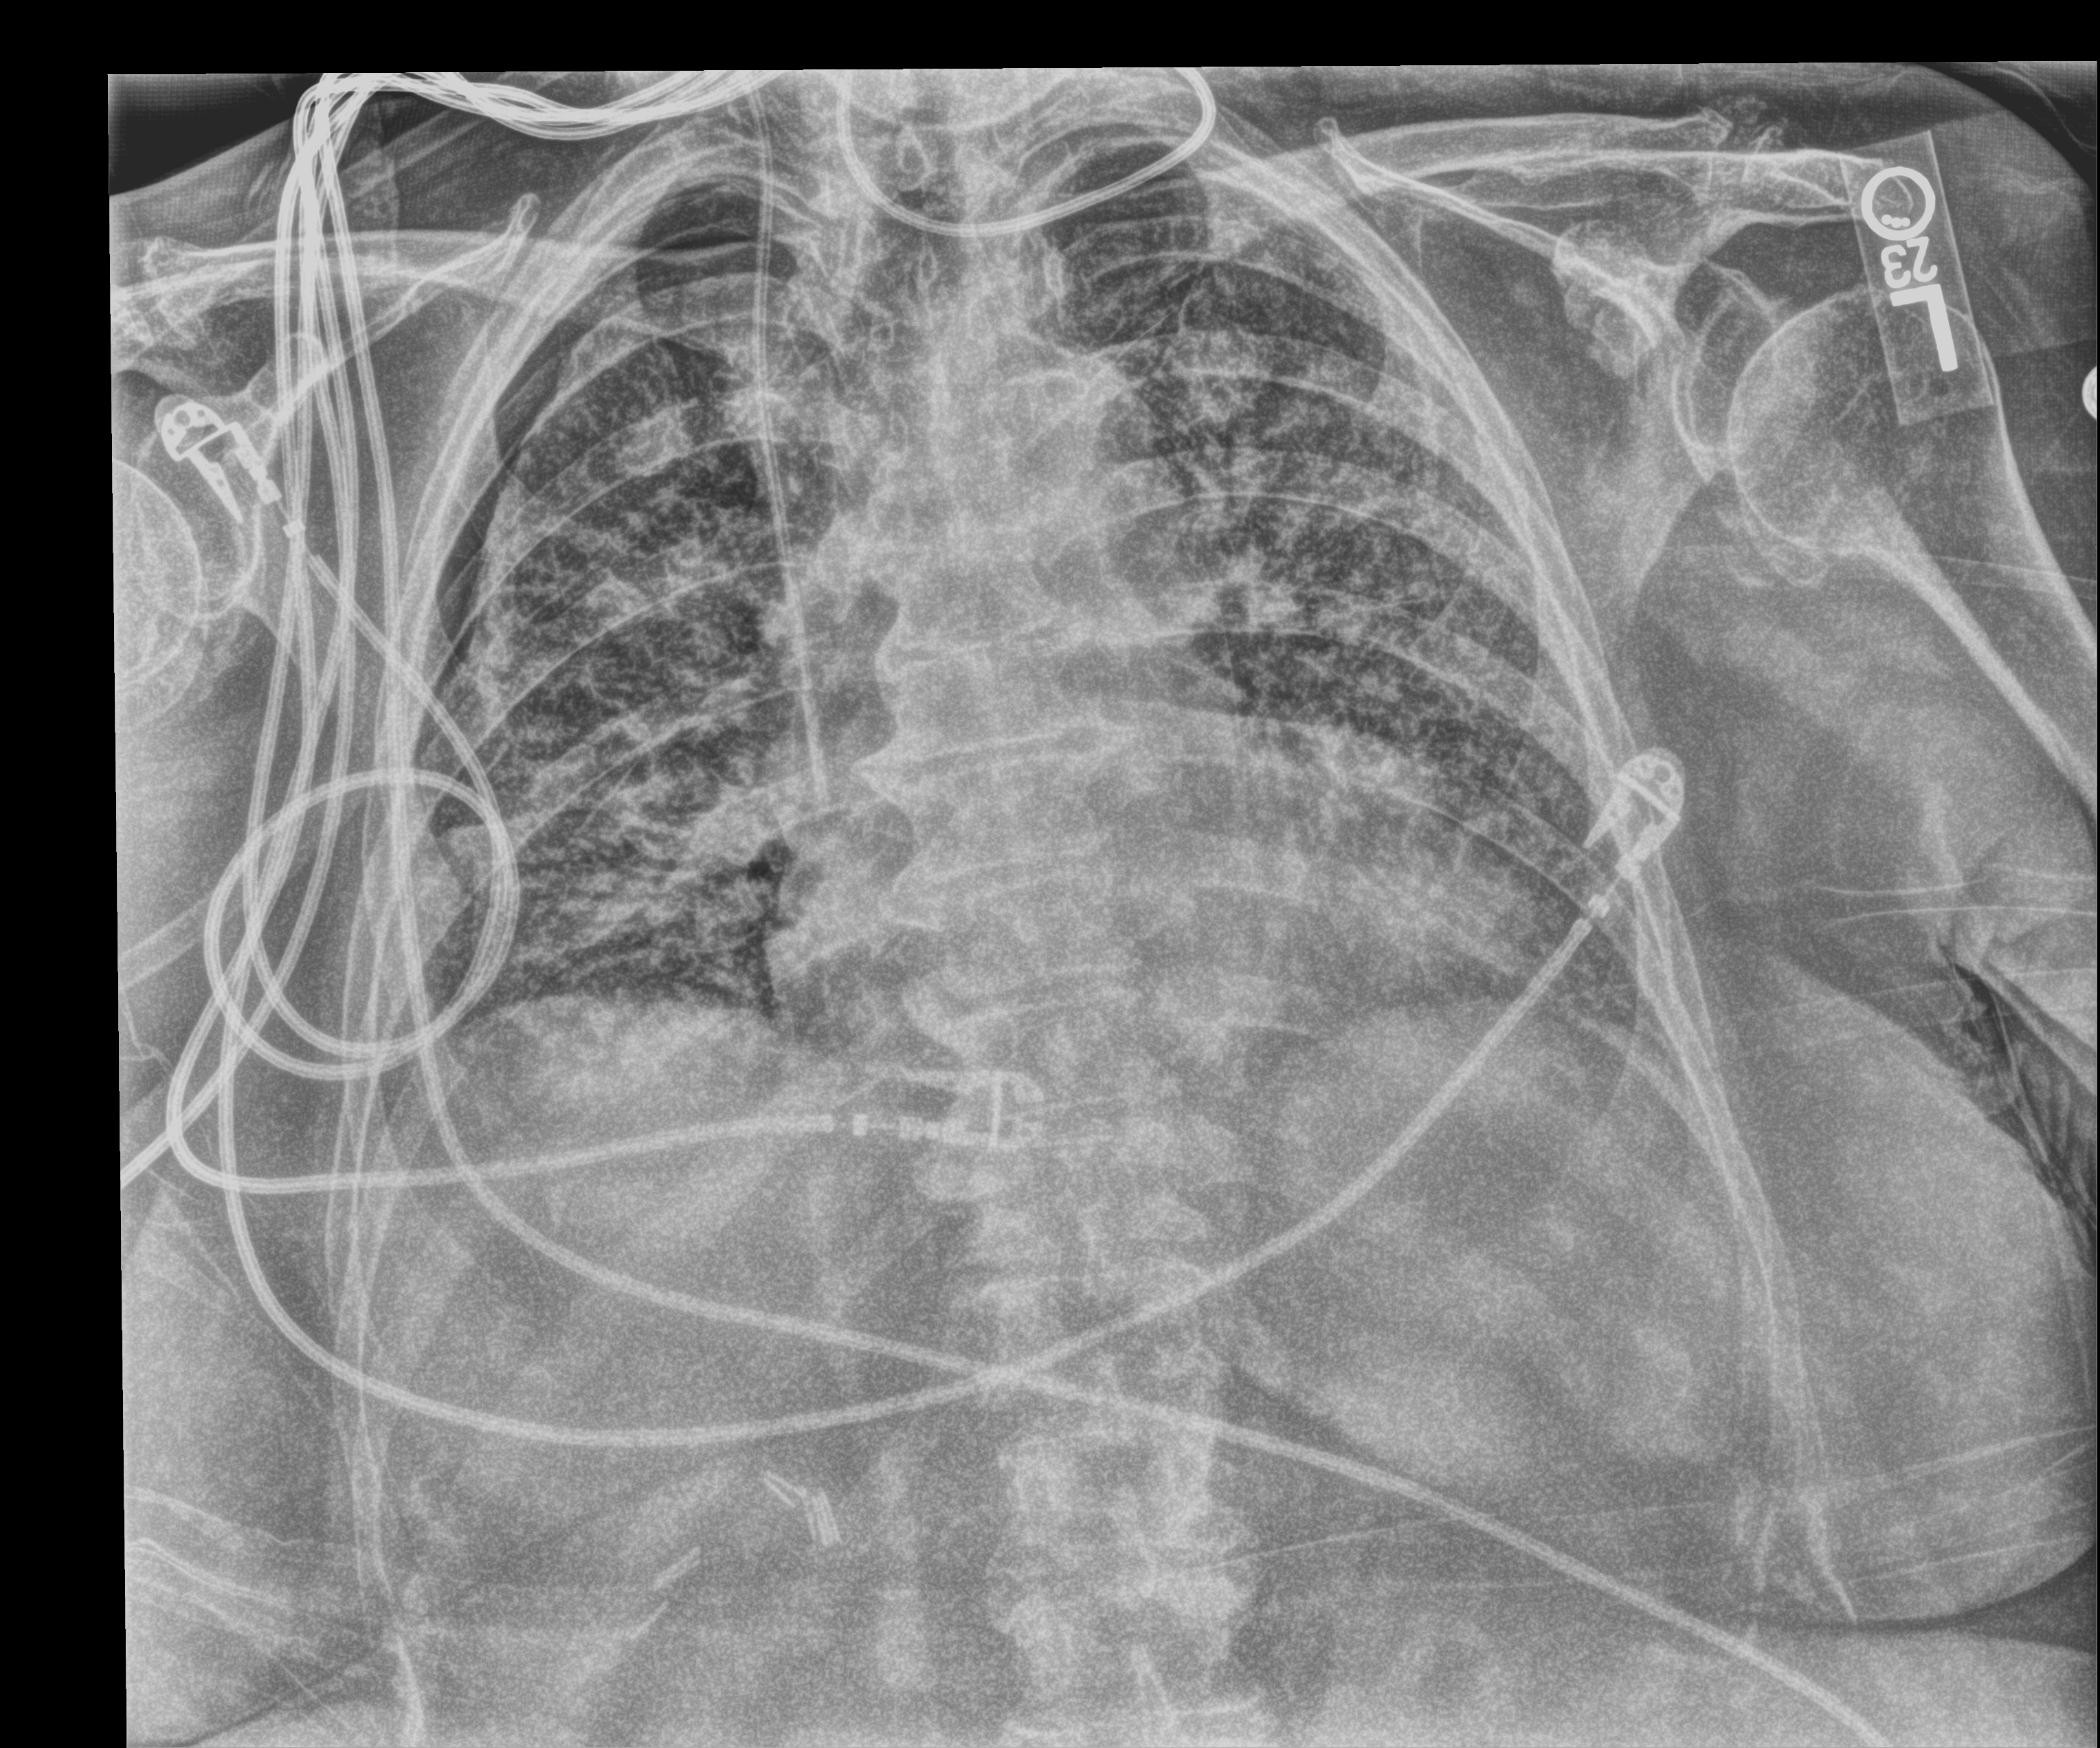
Bedside chest radiograph (computed radiography), anteroposterior (AP) projection. Female patient hospitalised with COVID-19, age 75–90 years.
Admission-level facts for this patient (not findings on this image; timing relative to this image not recorded):
- admitted to intensive care during this hospital stay: no